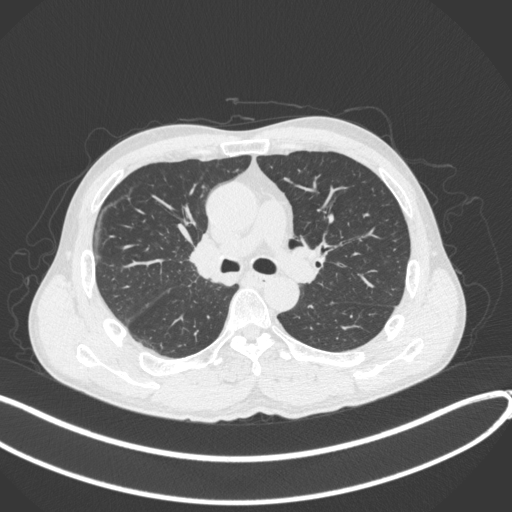
Chest CT, one axial slice; position 238 of 409 along the scan axis; 120 kVp; lung window (W 1500 / L -600 HU); 1 mm slice thickness; 512 × 512 image matrix, field of view 400 × 400 mm. Patient: male, 53 years. Case-level facts recorded for this patient, not image findings: clinical TNM (as recorded): T1b N0 M0.
Annotated regions visible in this slice (rectangle marked by the reading radiologist):
- lung tumour (recorded histology: squamous cell carcinoma): box from (x=187, y=231) to (x=224, y=284) px